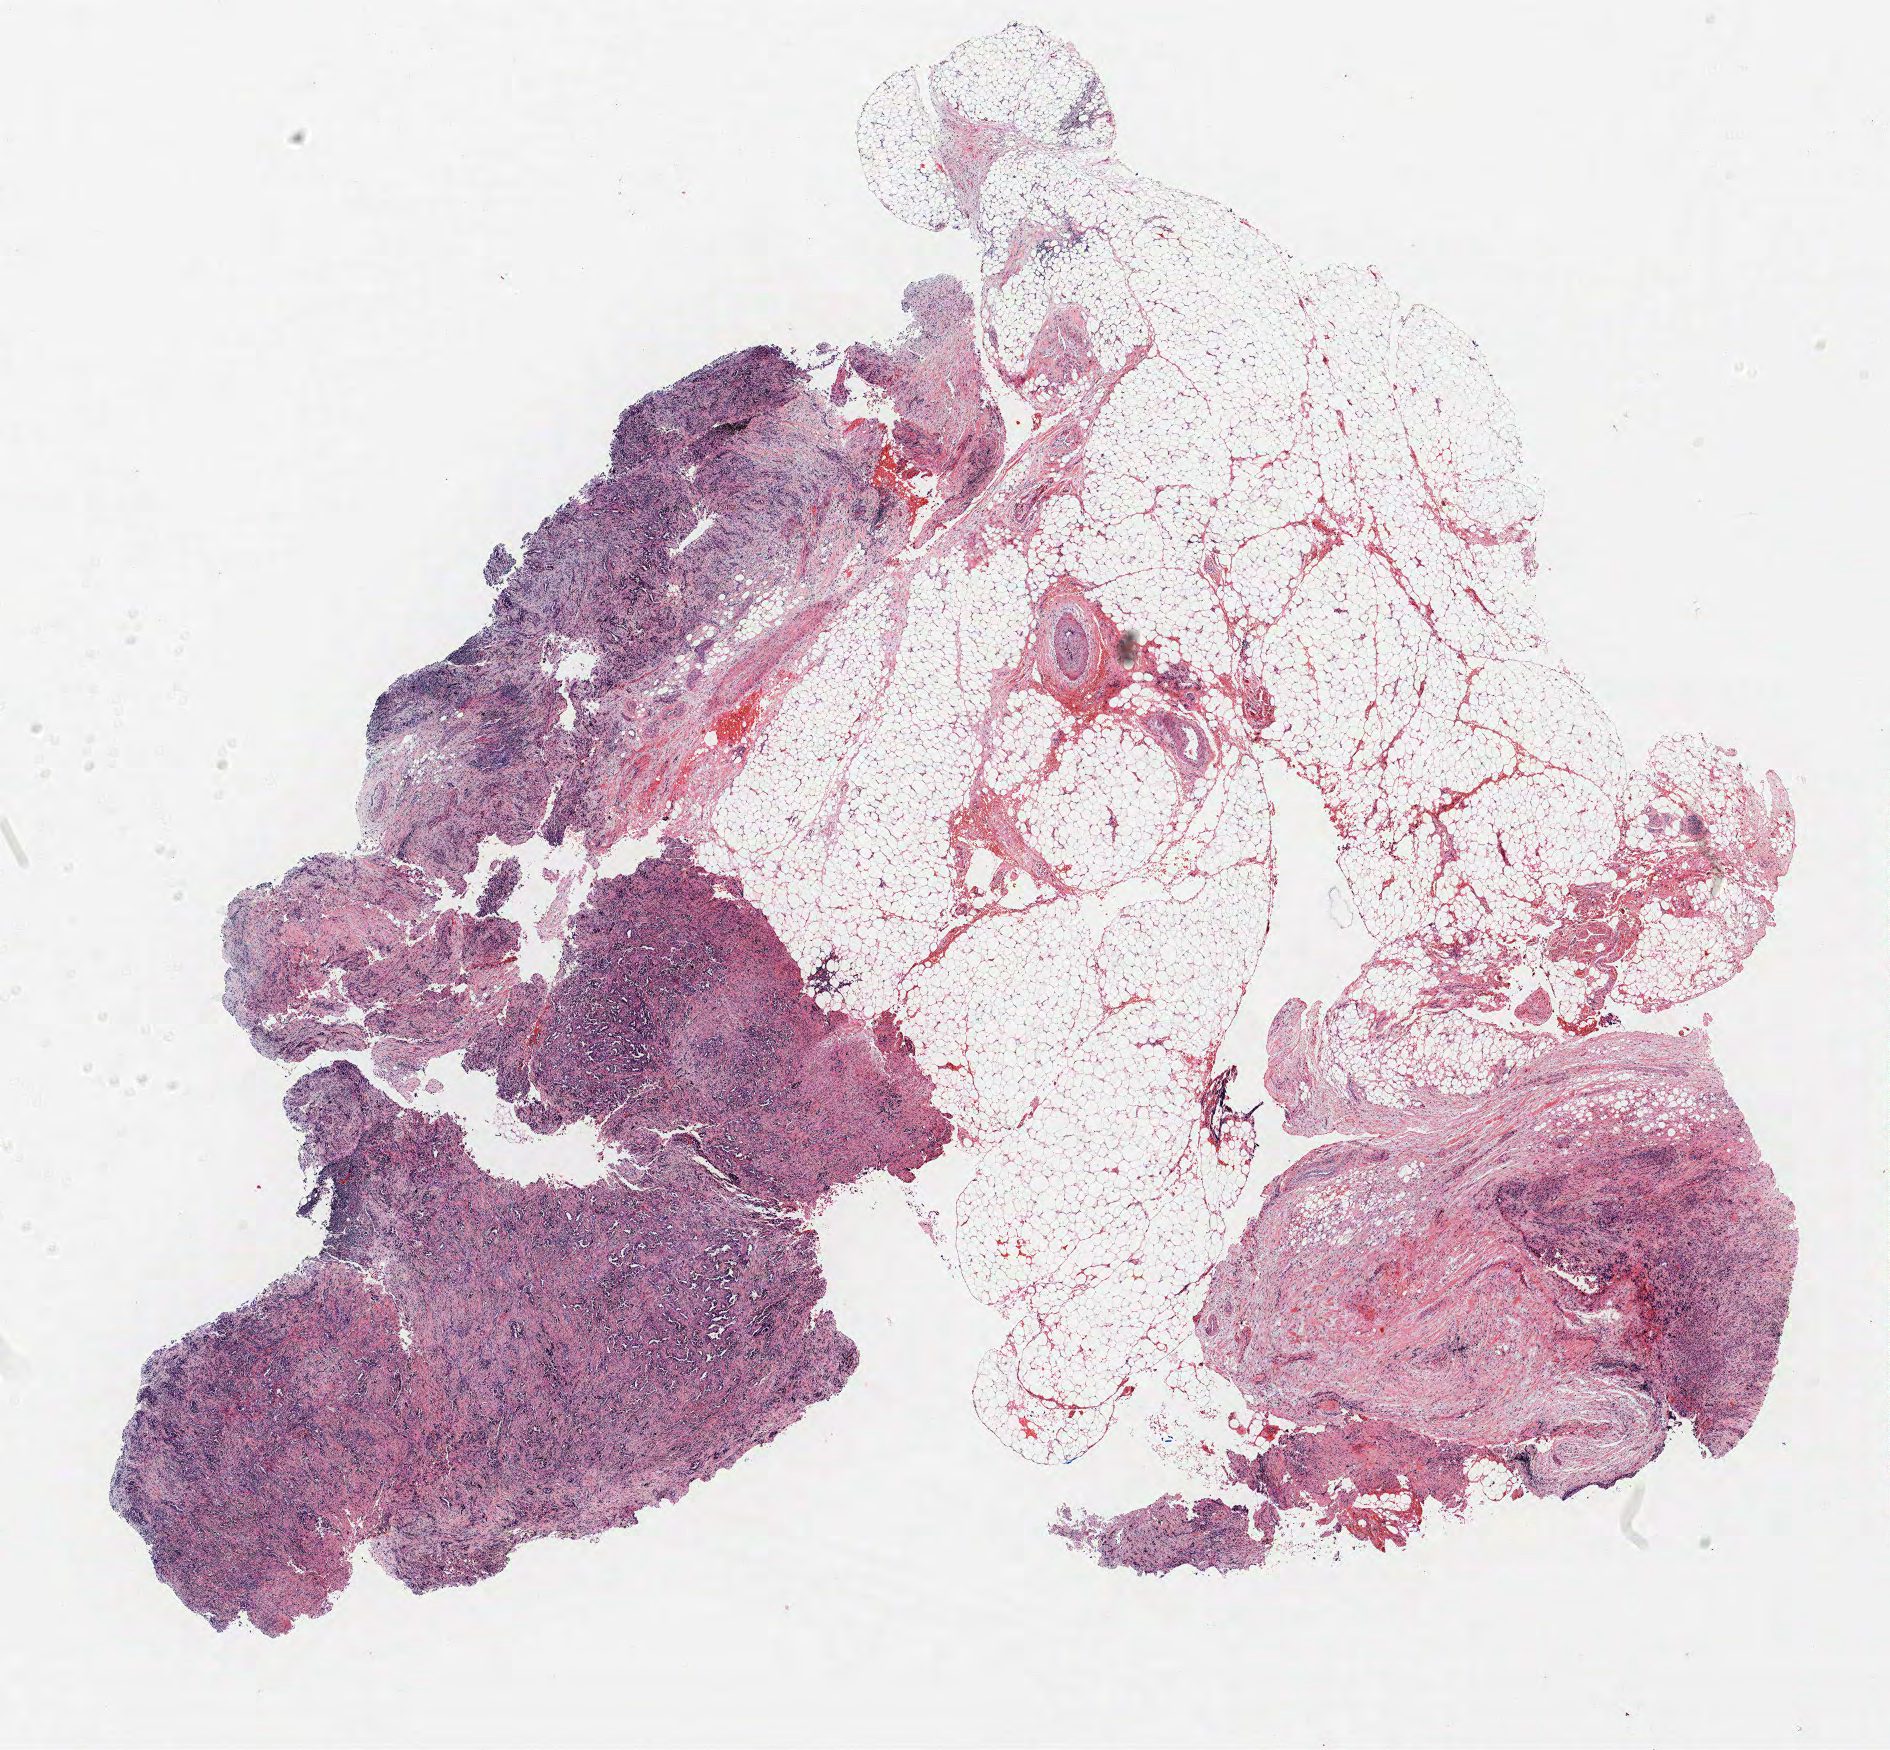
Whole-slide histology image, H&E-stained — low-resolution overview of the scanned area, about 15.1 x 14.0 mm (from a 40x scan). FFPE section. Lung. Male patient, aged 60 at enrolment. Current smoker at enrolment.
• tumour size (pathology): 11 mm
• stage (AJCC 6th edition): IA
• primary tumour location (clinical record): right upper lobe
• participant's lung-cancer diagnosis: Adenocarcinoma, NOS (ICD-O-3 8140/3)